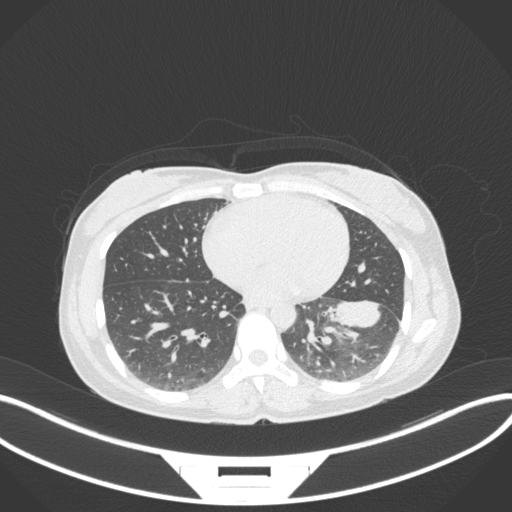
Chest CT, one axial slice. Slice 143 of 361 in the series (ordered by position). Reconstruction kernel B31f. Lung window (W 1500 / L -600 HU). 1 mm slice thickness. 512 × 512 image matrix, field of view 400 × 400 mm. Female patient, age 41 years. From the clinical record (not read from this slice): clinical TNM (as recorded): T2a N3 M1b.
Outlined on this slice (bounding box drawn by a radiologist):
- lung tumour (recorded histology: adenocarcinoma): bounding box [x1, y1, x2, y2] px = [319, 293, 389, 334]